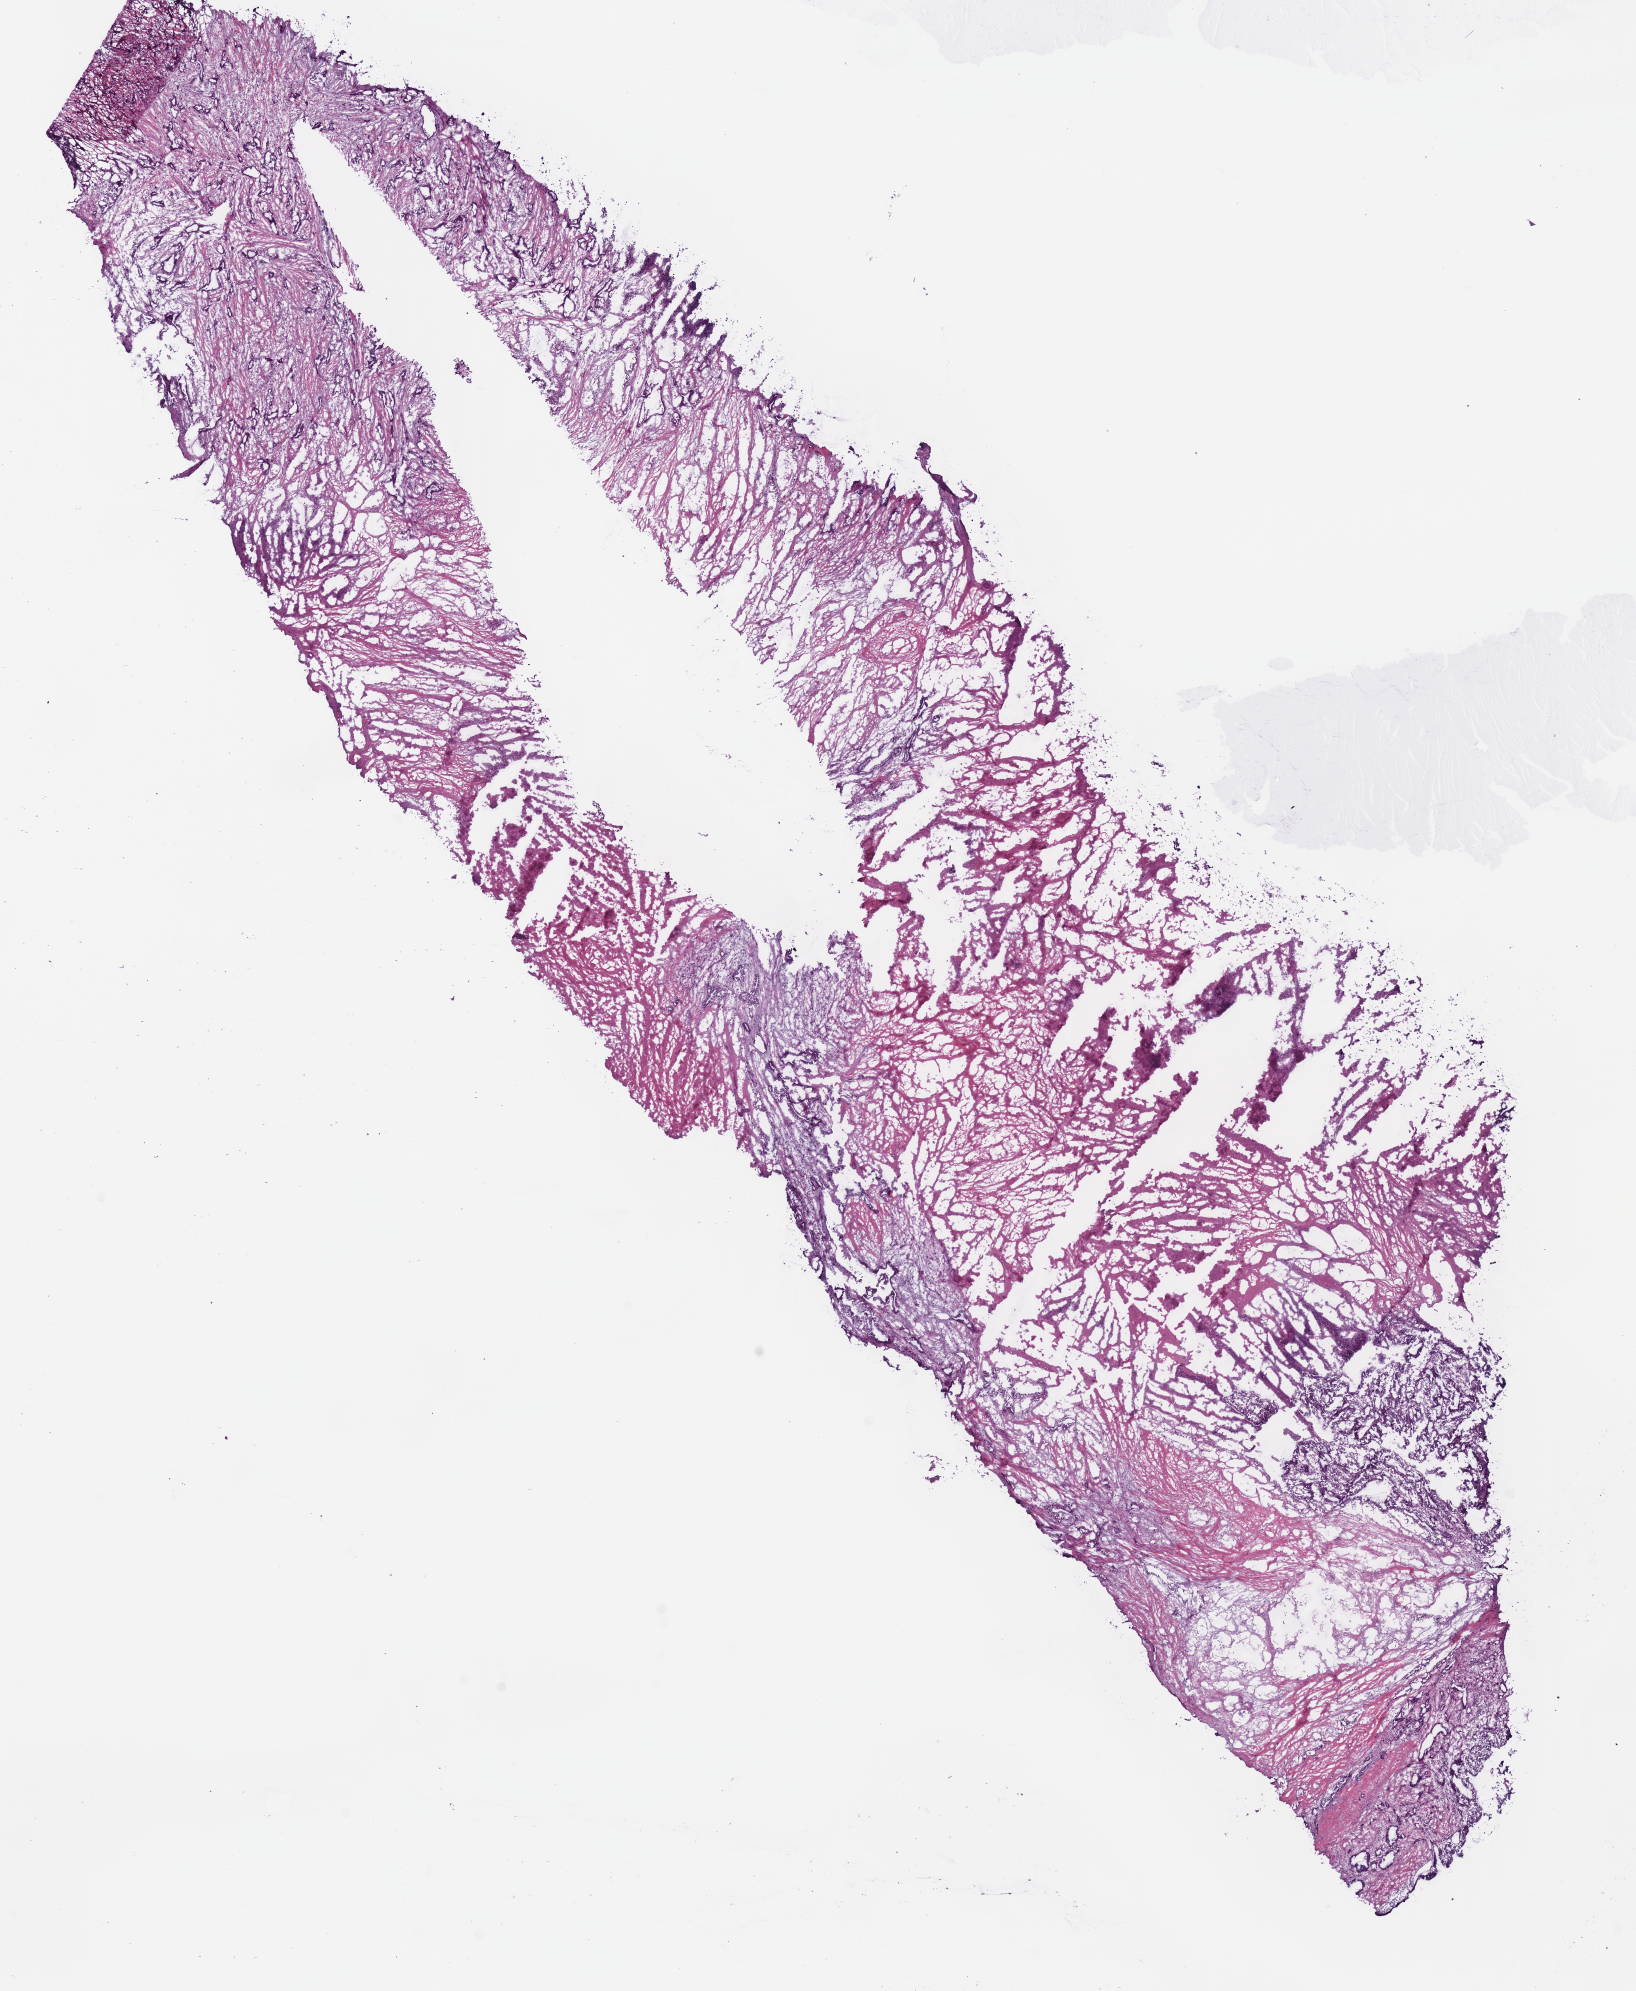
H&E-stained whole-slide image — whole scanned area (about 12.9 x 15.7 mm) shown as a low-resolution overview. Frozen section from the bottom of the tissue portion. Pancreas, primary tumour sample. Female patient; age at initial diagnosis 62 years. Histologic grade: G2 (moderately differentiated). Pathologist review of this section (percent, as recorded): tumour cells 50%, tumour nuclei 65%, normal cells 0%, stromal cells 25%, necrosis 25%.
TNM: T3 N1 M0. Lymph nodes positive (case pathology): 3 of 8 examined. Histologic diagnosis: Infiltrating duct carcinoma, NOS. AJCC pathologic stage: IIB.